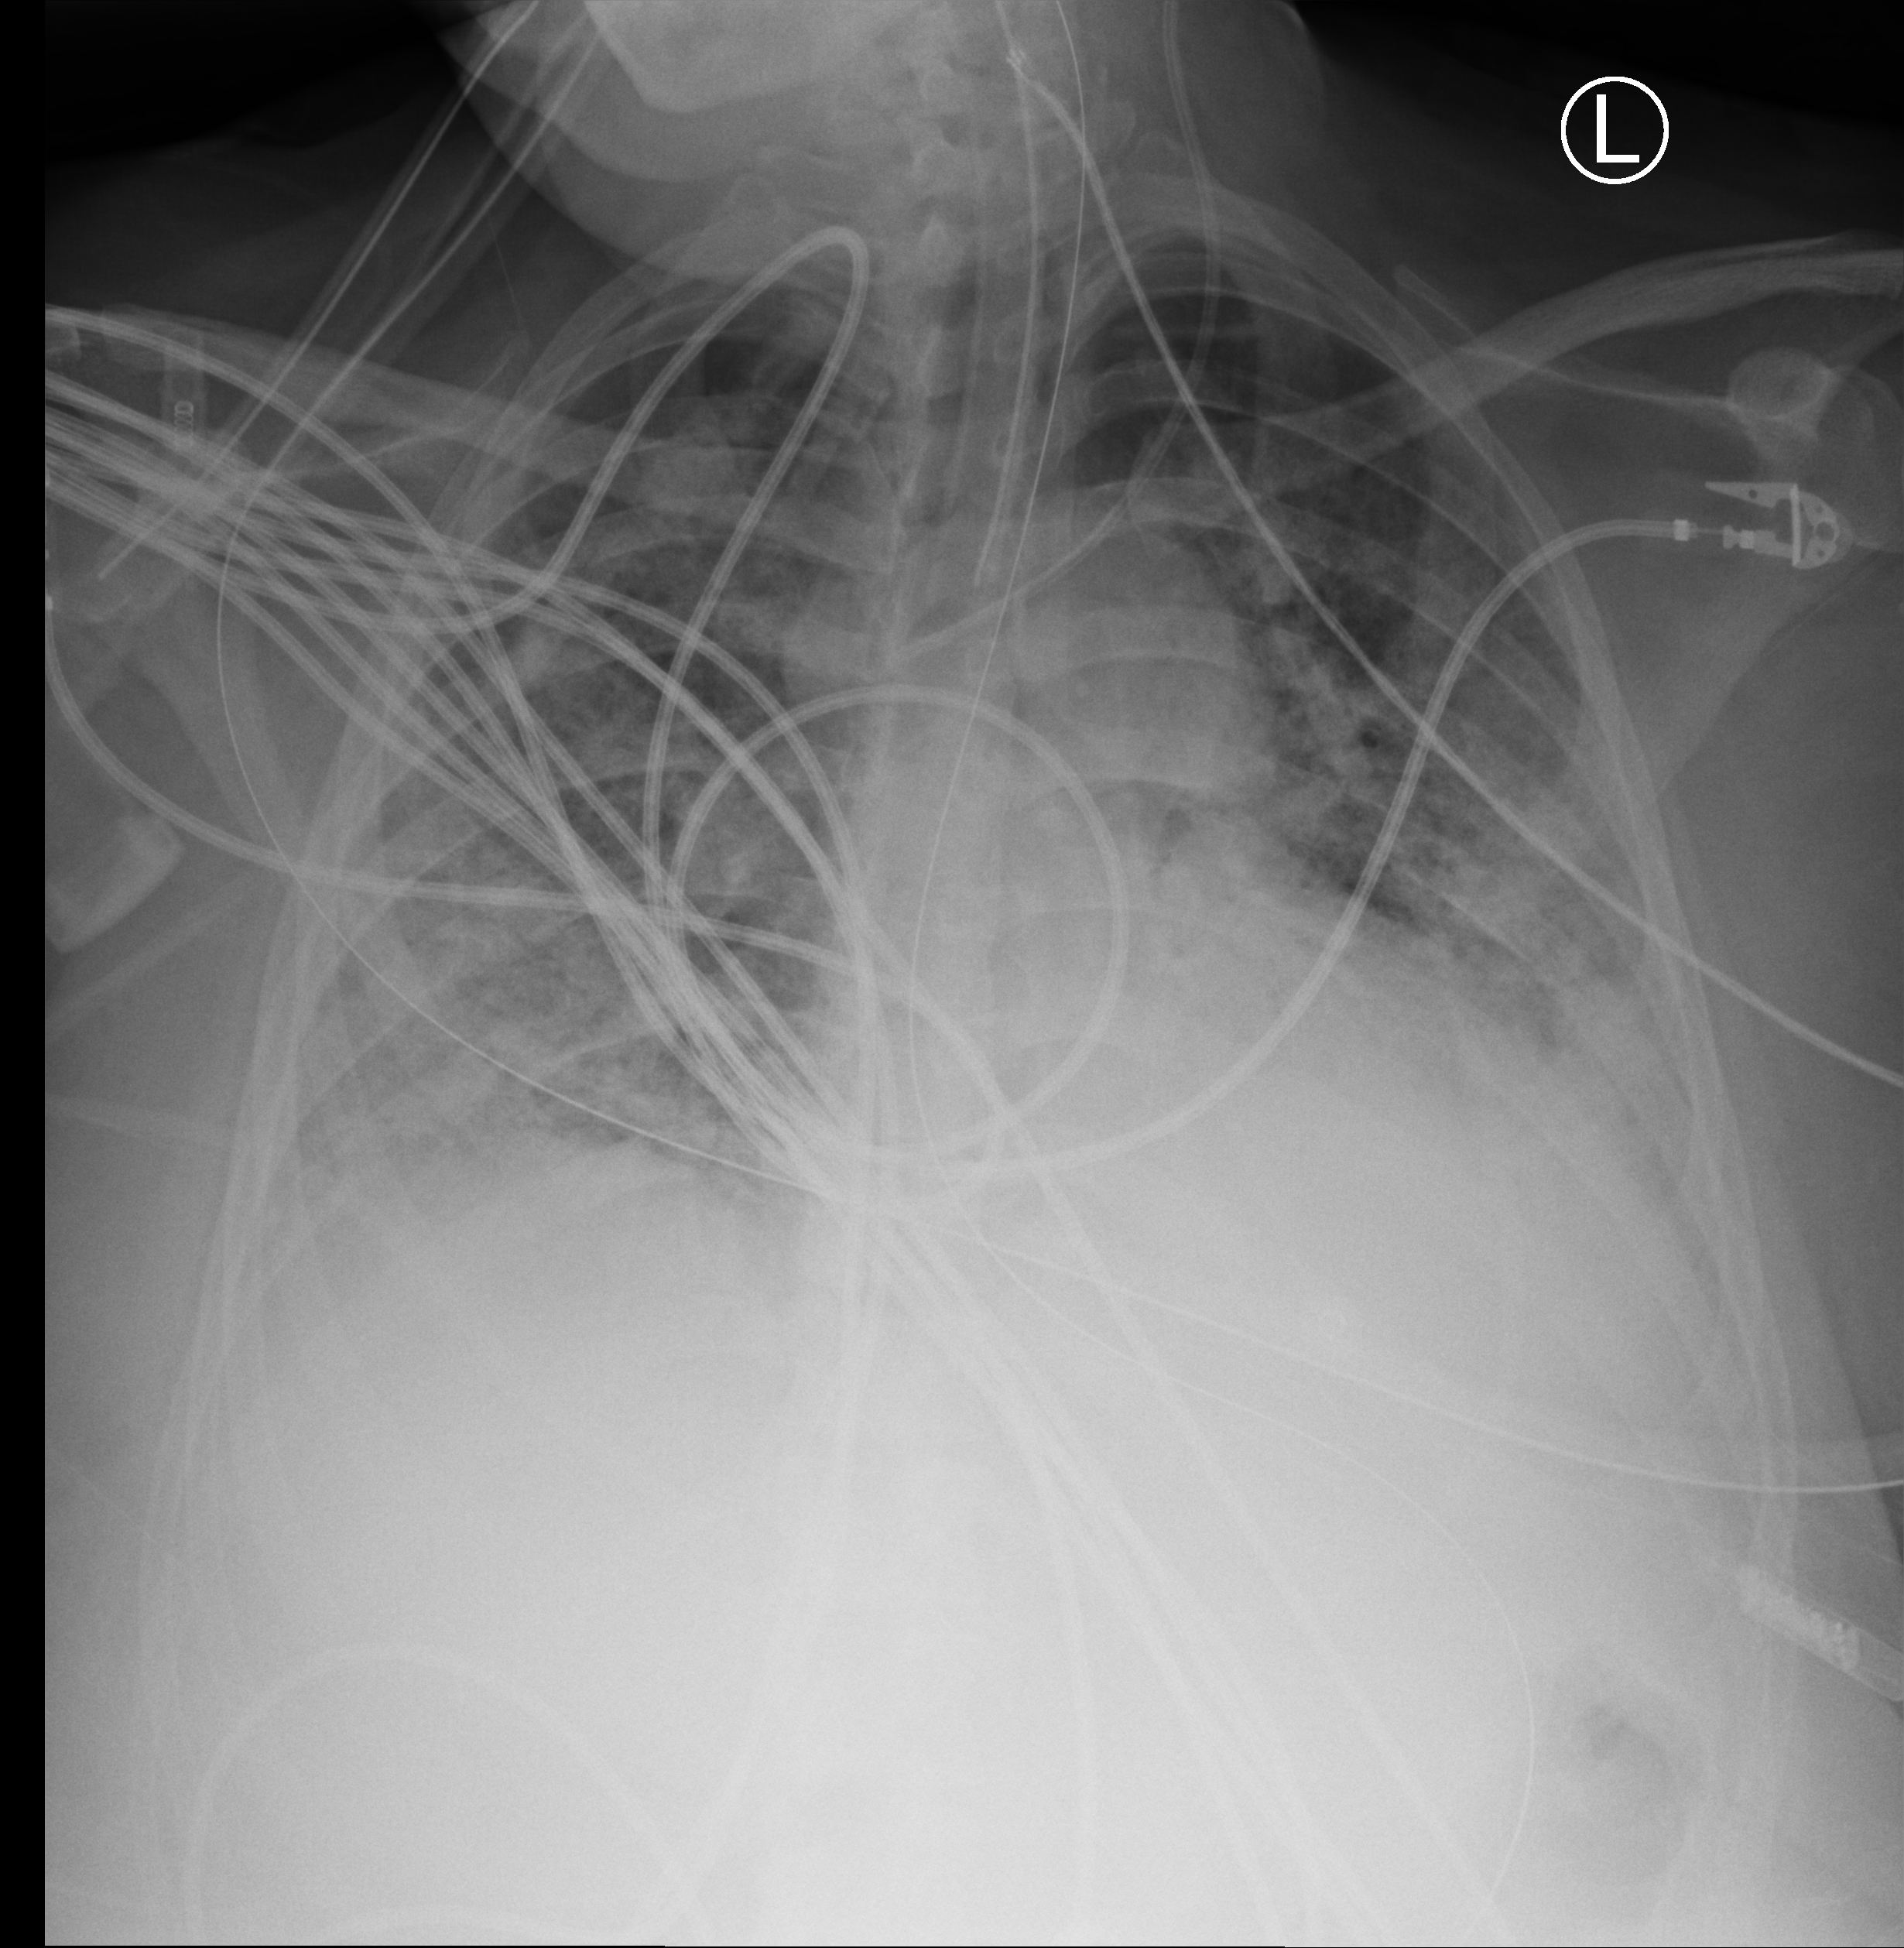
Bedside chest radiograph (computed radiography), anteroposterior (AP) projection. Patient hospitalised with COVID-19; female, aged 18–59 years.
From the hospital-stay record, not from the radiograph (when in the stay this image was taken is not recorded):
- admitted to intensive care during this hospital stay: no